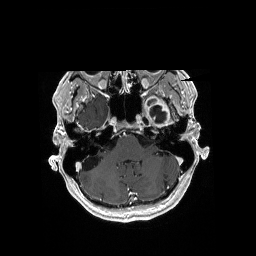
Brain MRI from a brain-tumour surgery series, one axial slice; slice 136 of 176 in the series (ordered by position); T1-weighted post-contrast; 256 × 256 image matrix, field of view 256 × 256 mm. Case-level facts recorded for this patient, not image findings: histopathology: Glioblastoma; WHO grade: 4; IDH mutation: no; tumour location: Left Medial Temporal.
Annotated regions visible in this slice (expert manual segmentation):
- previous resection cavity: bounding box (x1, y1, x2, y2) in pixels: (150, 106, 167, 121)